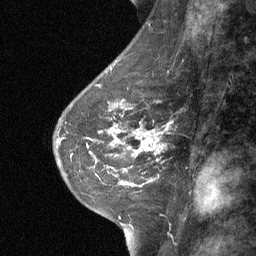
Breast MRI (dynamic contrast-enhanced), one sagittal slice. Dynamic contrast-enhanced study with each time point stored as its own series, time point 2 of 3 at this slice position (early post-contrast, ordered by acquisition time). 1.5 T. TE 4.8 ms, TR 27 ms. 2 mm slice thickness. 256 × 256 image matrix. Female patient, age 42 years. From the clinical record (not read from this slice): setting: breast cancer imaged before/during neoadjuvant chemotherapy; receptor status: triple-negative.
Annotated regions visible in this slice (semi-automatic segmentation, software-assisted and operator-edited):
- analysis volume of interest (the breast-tissue region the enhancement analysis was run in; not a lesion): box from (x=99, y=117) to (x=173, y=187) px
- tumour enhancement mask (voxels above the 90 % enhancement threshold inside the analysis volume of interest): (x=113, y=125)–(x=169, y=186)